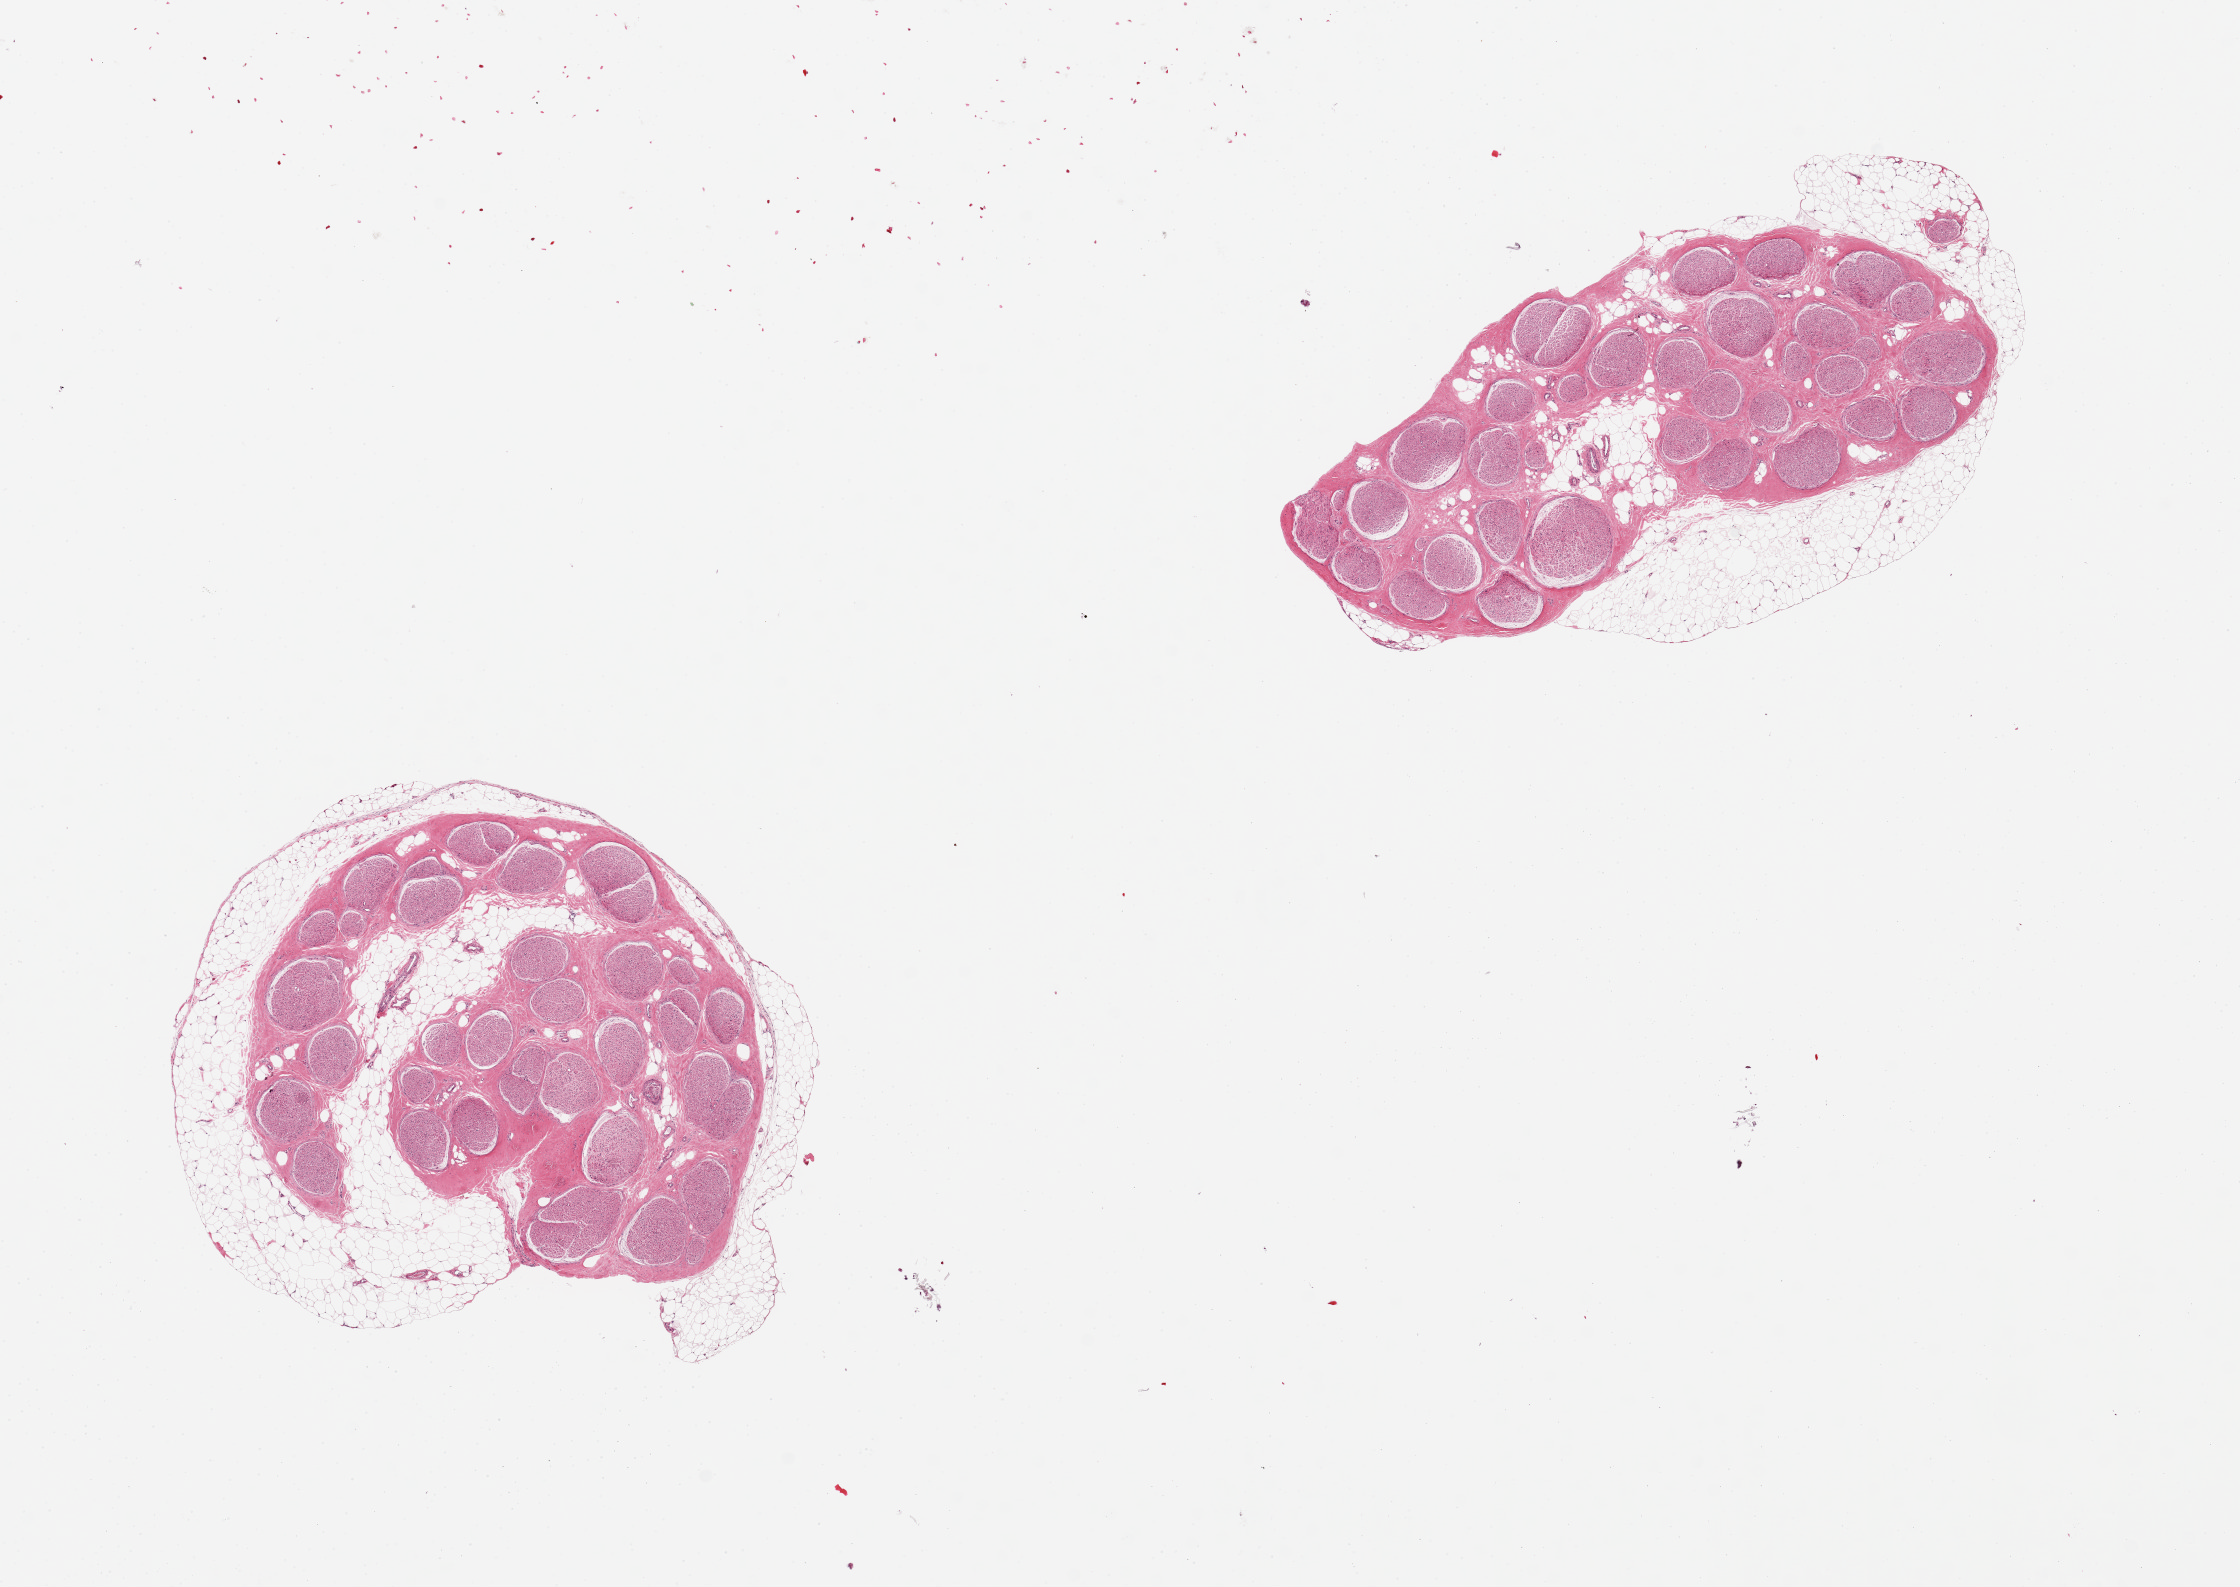
Digitized haematoxylin and eosin-stained section, brightfield — shown as a low-resolution overview of the whole scanned area (about 17.7 x 12.6 mm, acquisition: 20x scan); PAXgene-fixed paraffin-embedded (PFPE) section; section of tibial nerve (target tissue); tissue donor sample. Donor: female.
• pathologist's review note for this sample: 2 pieces, rims of discontinuous fat up to 1mm